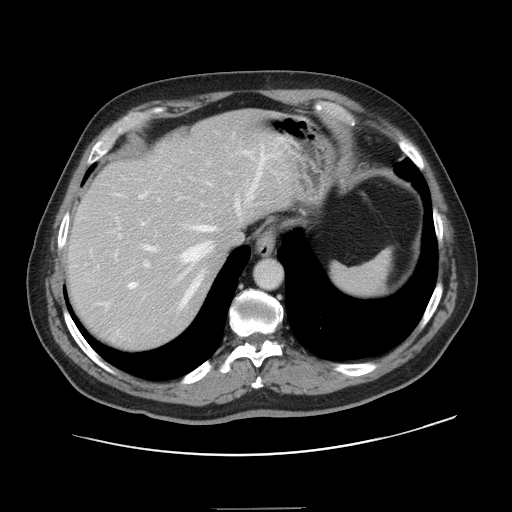
Contrast-enhanced abdominal CT, one axial slice. Position 115 of 143 along the scan axis. 120 kVp. Intravenous contrast given. Soft-tissue window (W 400 / L 40 HU). 2.5 mm slice thickness. 512 × 512 image matrix, field of view 402 × 402 mm. Male patient, age 62 years. Case-level facts recorded for this patient, not image findings: diagnosis: colorectal cancer liver metastases, imaged before liver resection; multiple liver metastases: yes; largest metastasis: 2.7 cm; disease in both lobes: no.
Outlined on this slice (manually delineated by an expert):
- hepatic veins: bounding box [x1, y1, x2, y2] px = [106, 151, 264, 306]
- liver: [68, 114, 298, 351]
- planned liver remnant (the part of the liver to remain after resection): [68, 114, 297, 284]
- portal vein (with intrahepatic branches): [119, 157, 265, 267]